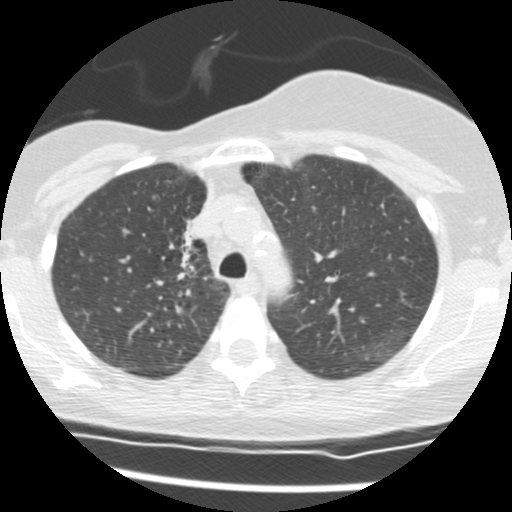
Axial slice from a low-dose chest CT screening exam; second screening round (one year after baseline); lung window (W 1500 / L -600 HU); 2.5 mm slice thickness; 512 × 512 image matrix, field of view 296 × 296 mm. Female, age 56 years at enrolment. Current smoker at enrolment.
• Expert-annotated lung lesion, box from (x=155, y=211) to (x=215, y=283) px.
• The screening reader recorded 2 non-calcified nodules or masses ≥4 mm on this exam (right middle lobe, right lower lobe); which of them this box marks is not recorded.
• Official screen result: positive, change unspecified: nodule(s) >= 4 mm or enlarging nodule(s), mass(es), or other non-specific abnormalities suspicious for lung cancer.
• Participant outcome: lung cancer diagnosed 675 days after this screen — adenocarcinoma, NOS, right upper lobe, stage IIIB (AJCC 6th edition), 8 mm at pathology.